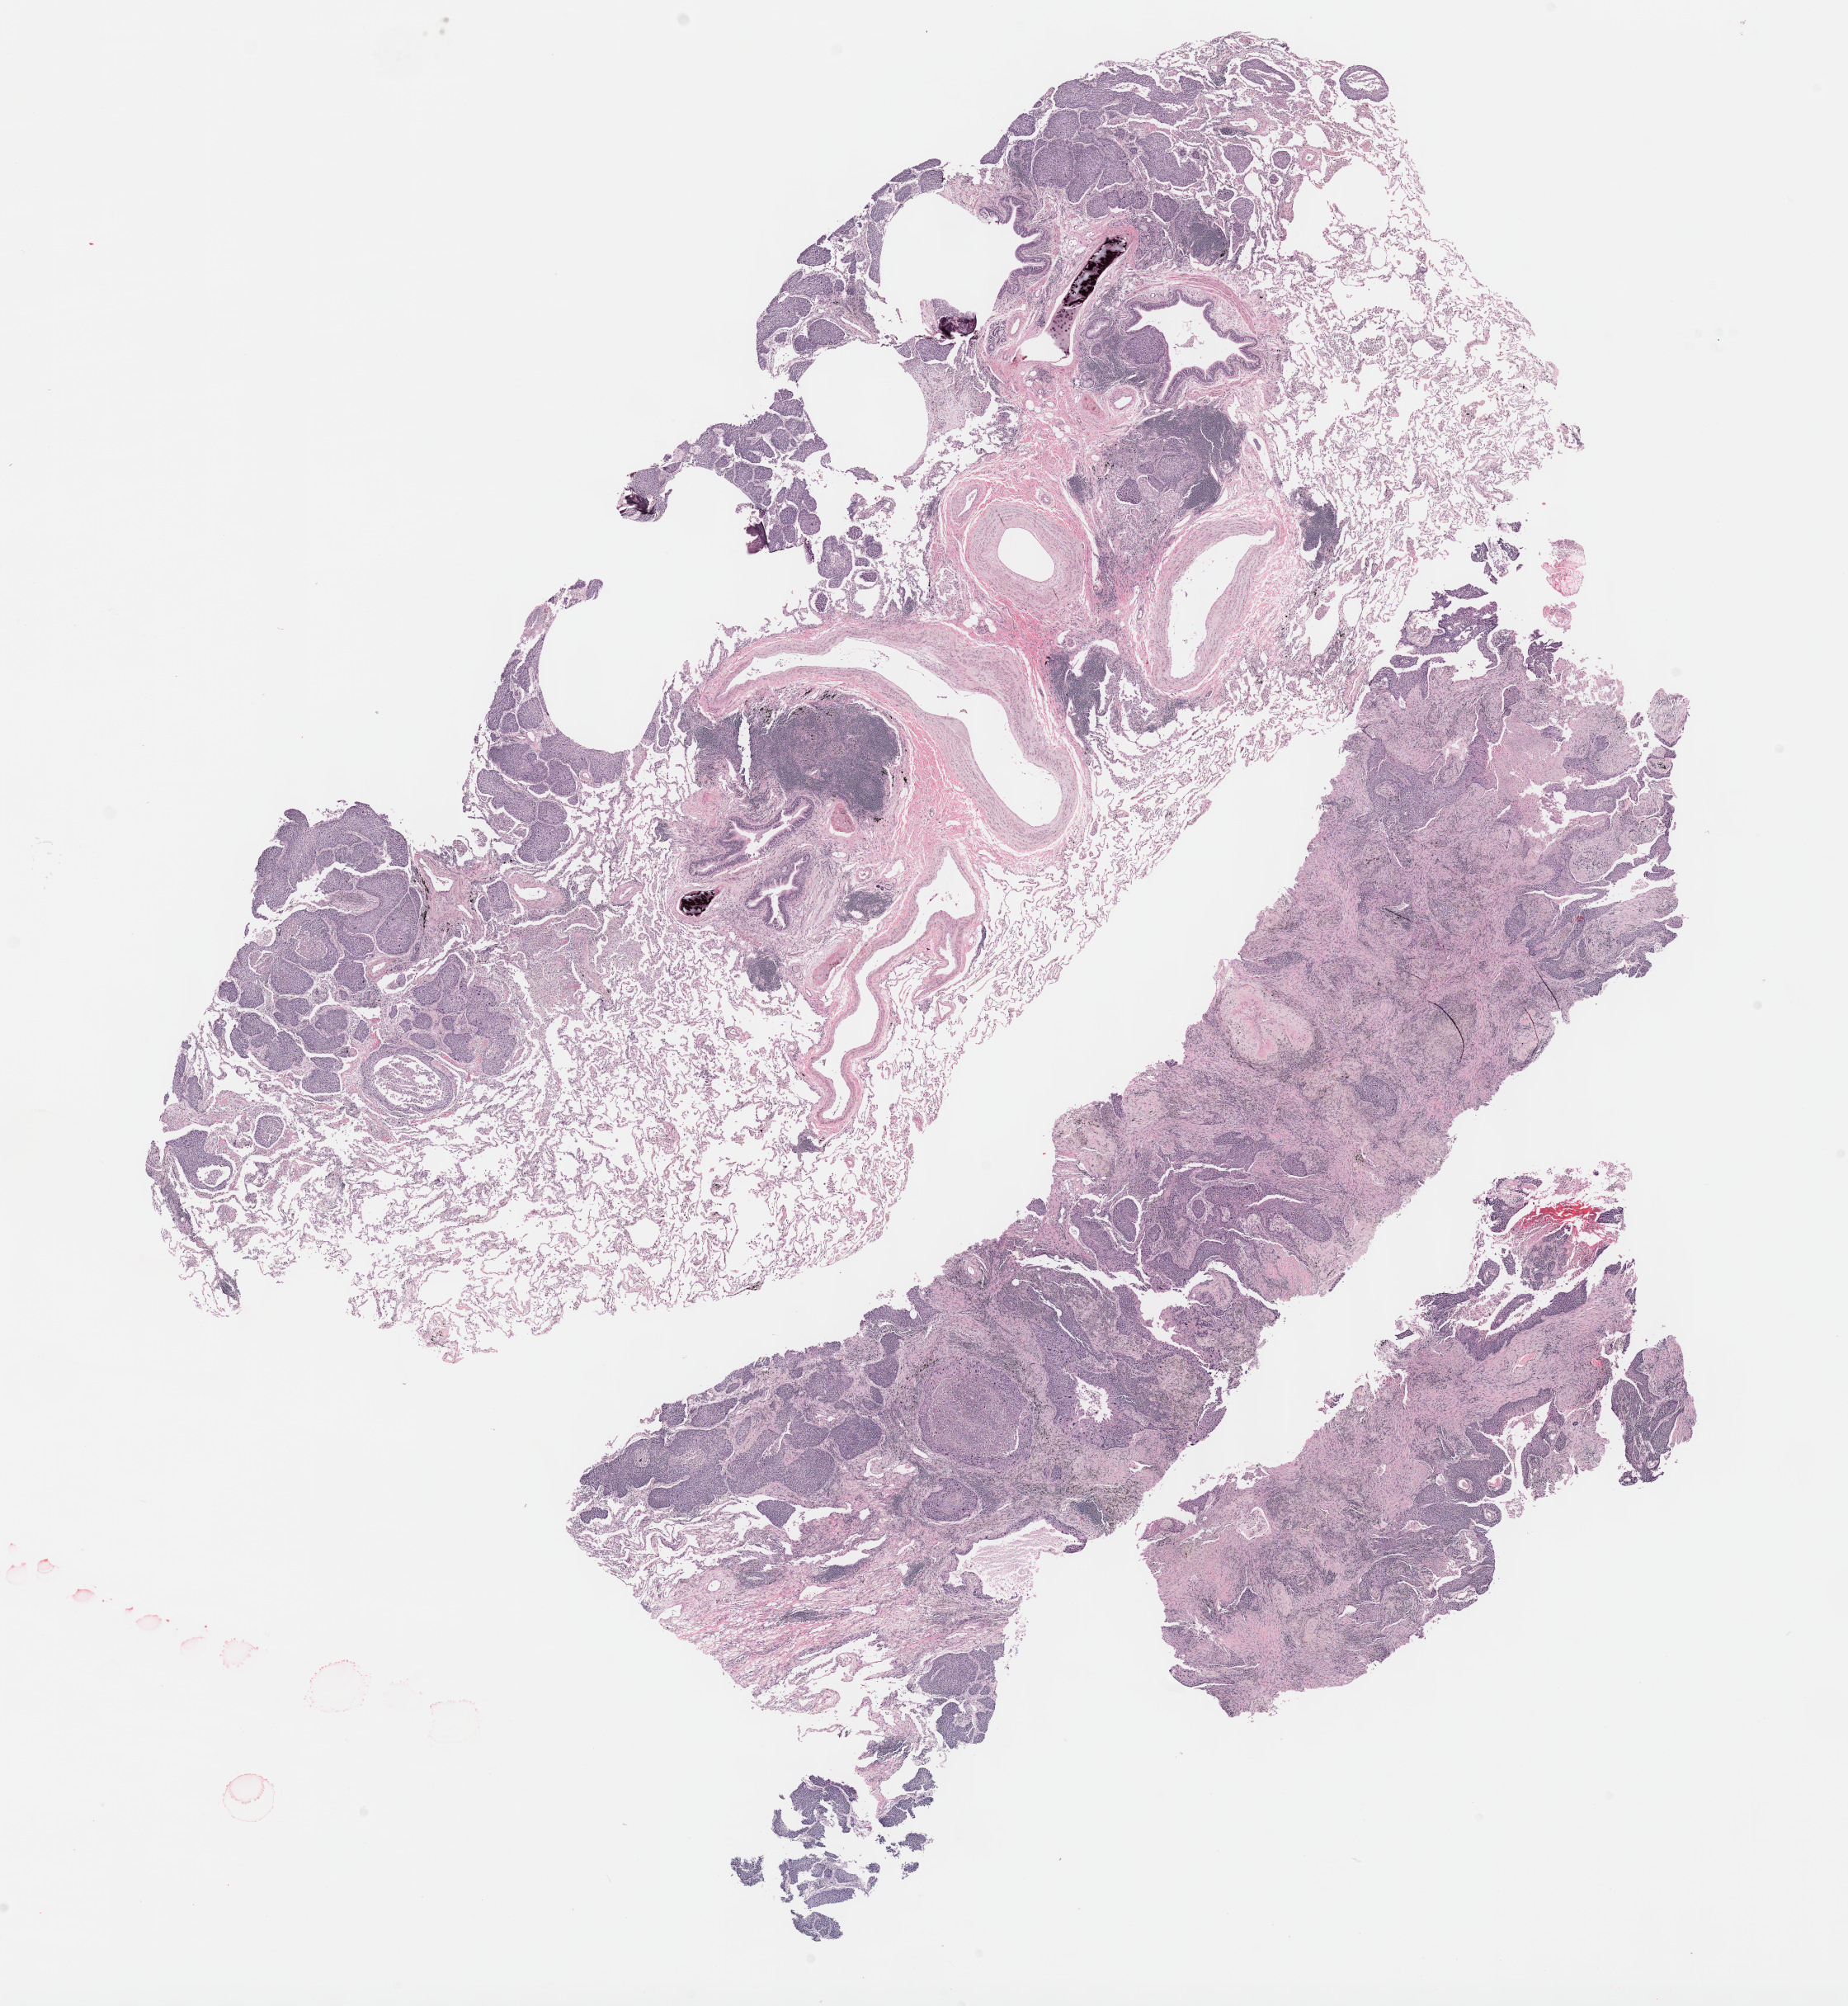
Whole-slide histology image, H&E, a low-resolution overview of the entire scanned area, about 18.1 x 19.7 mm. Formalin-fixed paraffin-embedded (FFPE) diagnostic section. Sample: primary tumour, lung. Patient: female, age at initial diagnosis 68 years.
AJCC pathologic stage: IB. Pathologic diagnosis: Squamous cell carcinoma, NOS (lower lobe, lung). Laterality: left.